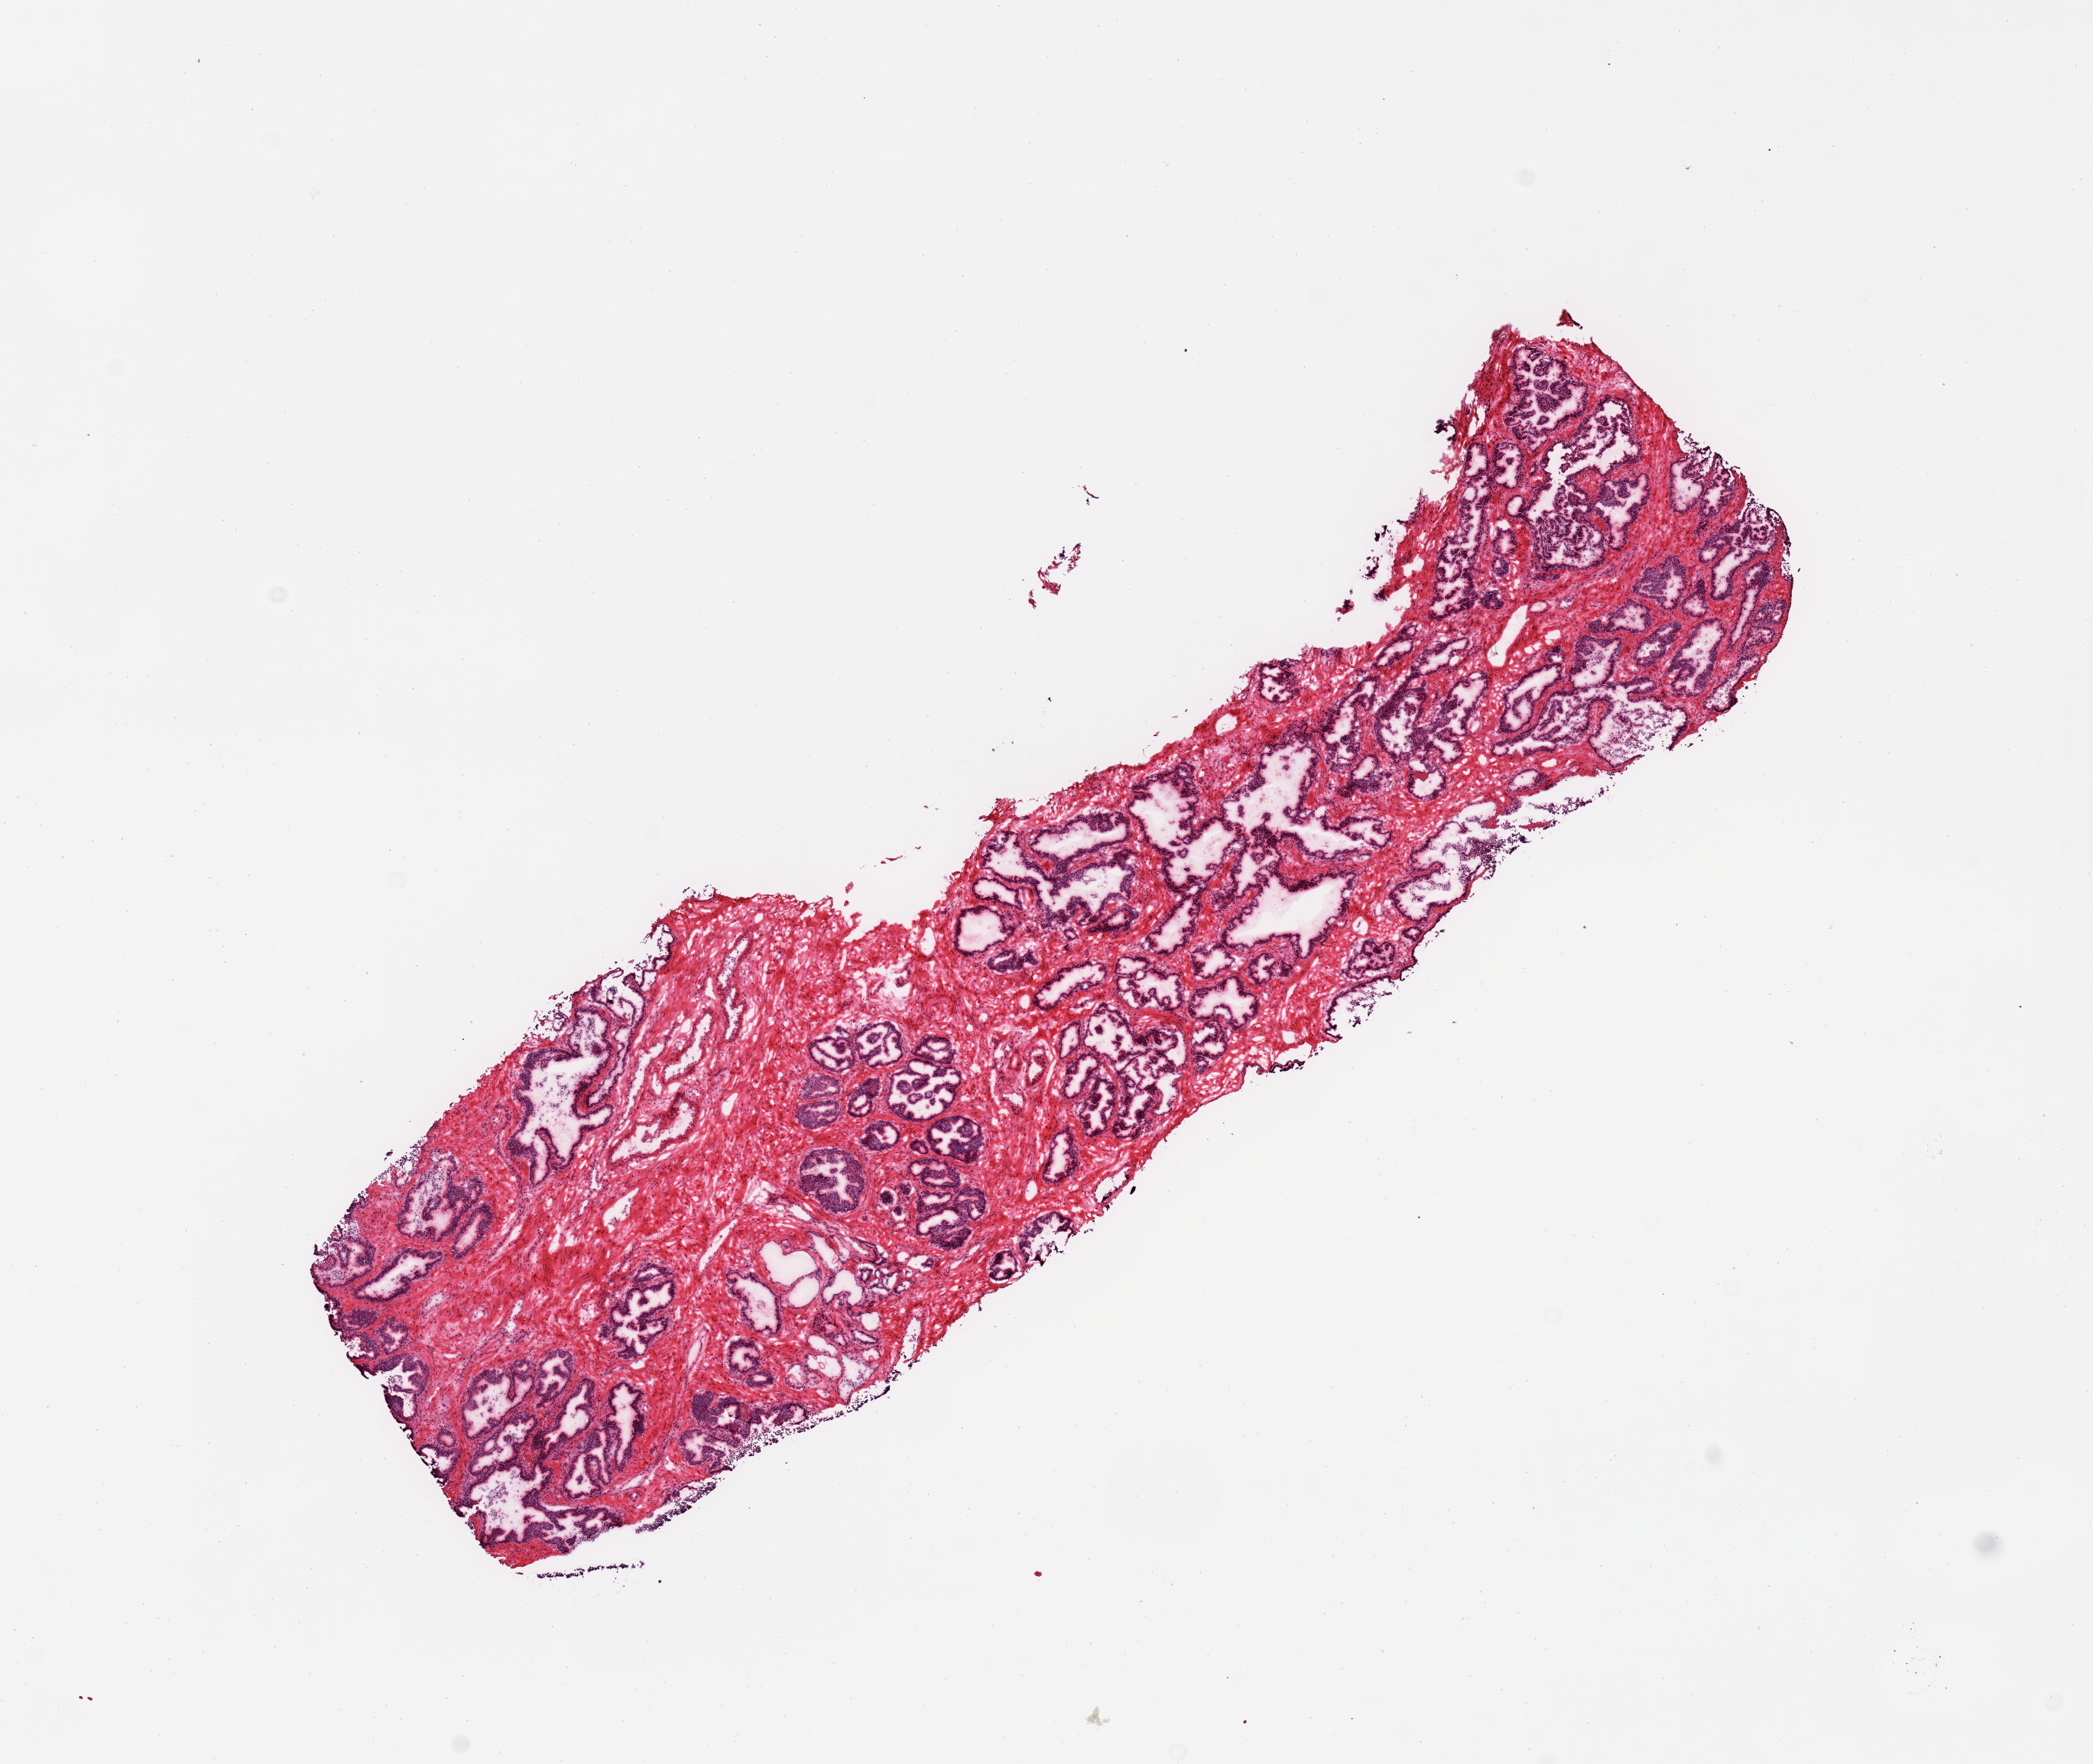
Digitized haematoxylin and eosin-stained section — a low-resolution overview of the entire scanned area, about 10.8 x 9.1 mm; frozen section (dry ice); sampled site (target tissue): esophageal muscle; donor tissue sample. Male donor.
• reviewer comment on this tissue sample: 1 piece; prostate sampled, not esophagus muscularis